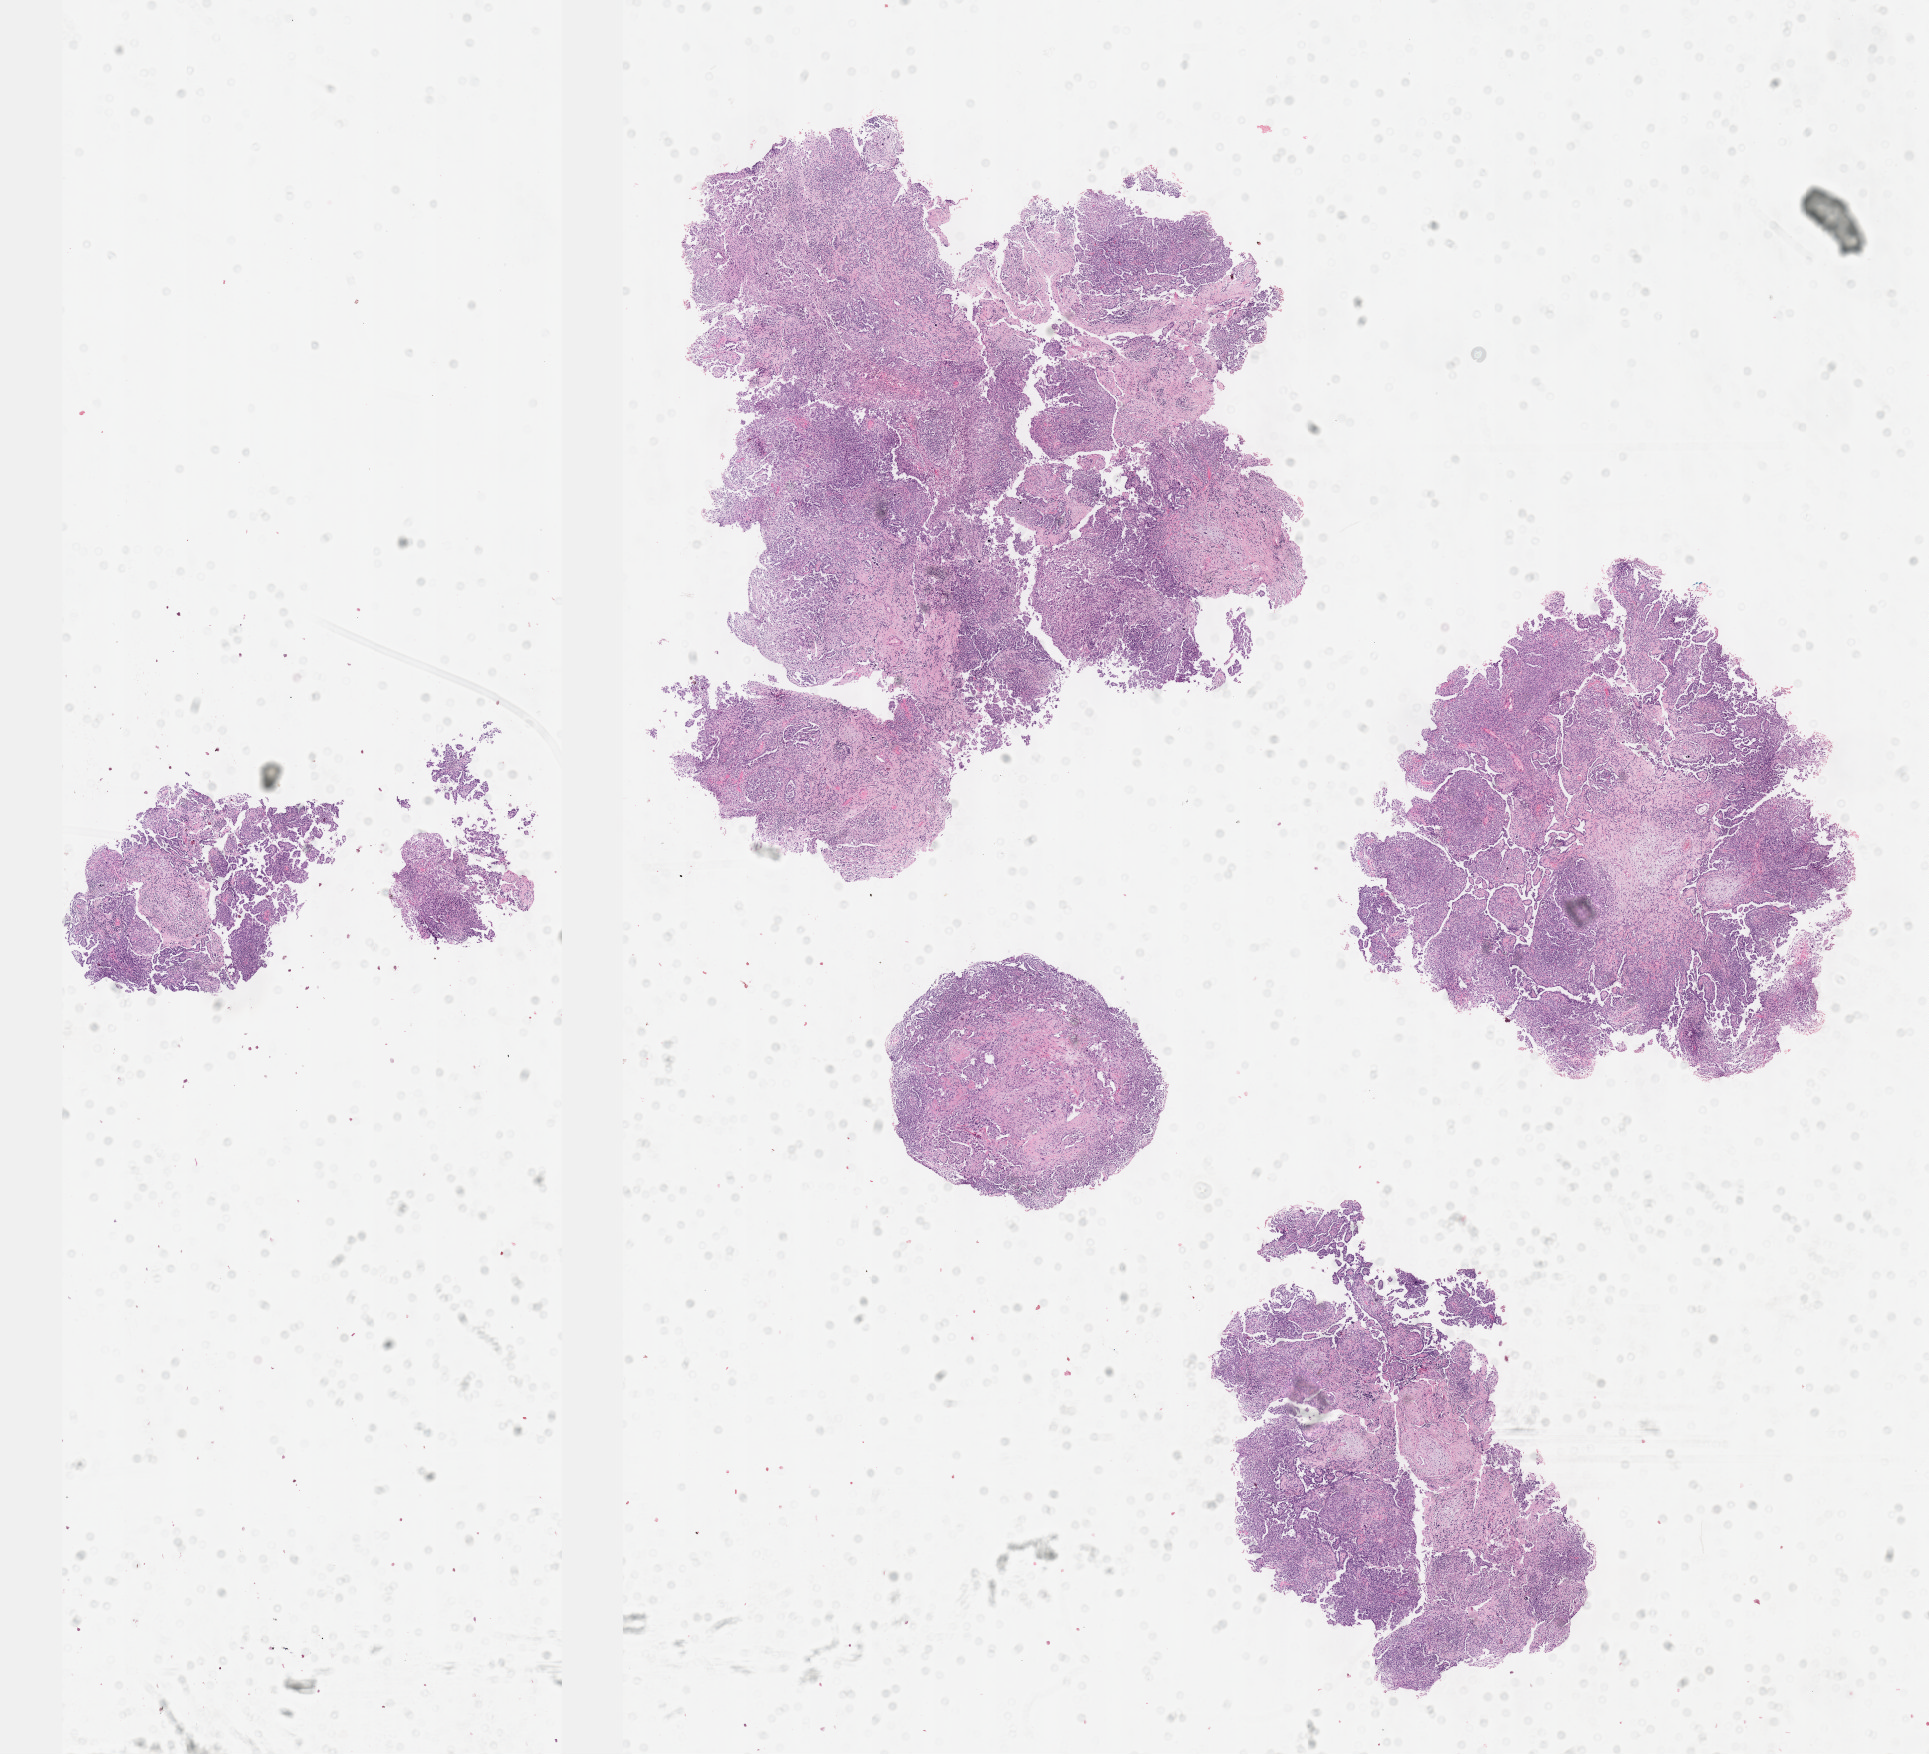
Digitized Hematoxylin and eosin (H&E) stained tissue section (whole slide) — low-resolution overview of the scanned area, about 15.6 x 14.2 mm (acquisition: 40x scan), formalin-fixed paraffin-embedded (FFPE) diagnostic section, mesothelium, primary tumour sample. Male patient; age at initial diagnosis 73 years.
Pathologic diagnosis: Mesothelioma, biphasic, malignant (pleura, NOS). AJCC pathologic stage: III (7th edition). TNM: T3 N0 M0.